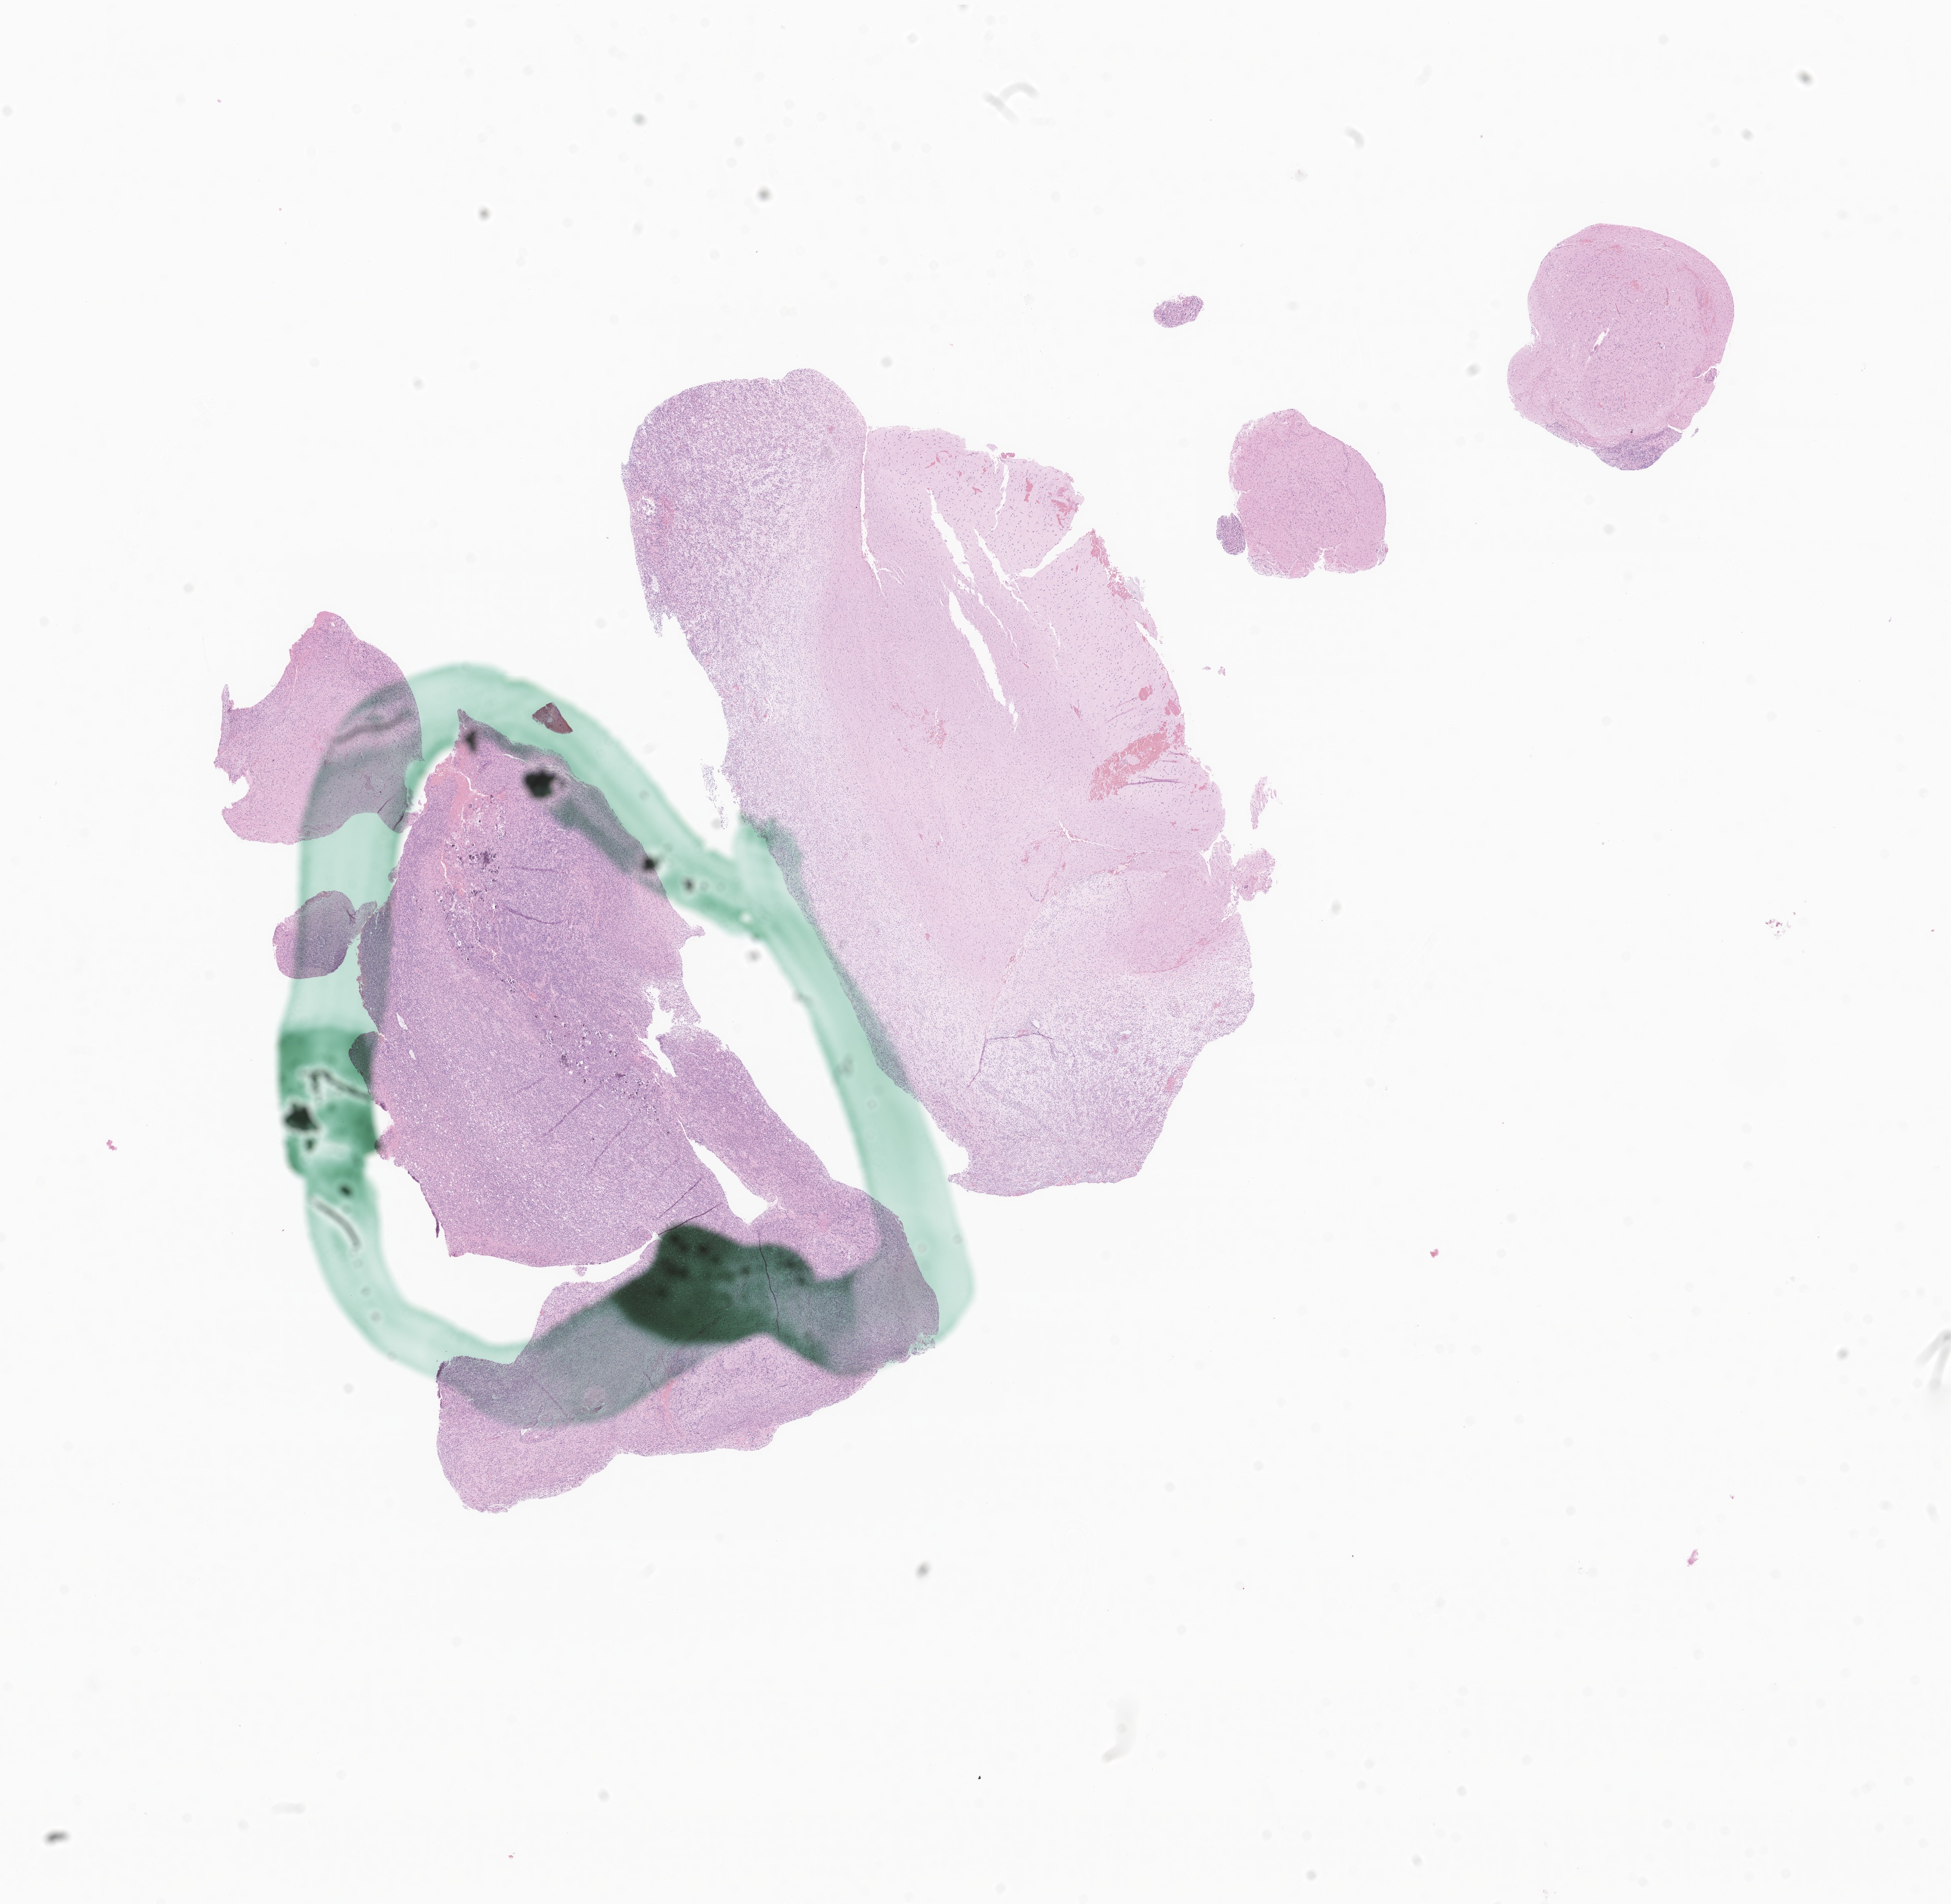
Whole-slide image, hematoxylin and eosin (H&E) stain of tumor tissue from the parietal lobe — shown as a low-resolution overview of the whole scanned area (about 16.9 x 16.5 mm); FFPE section. Patient: male, age 187 months.
- diagnosis (ICD-O-3 morphology term): Olfactory neurocytoma